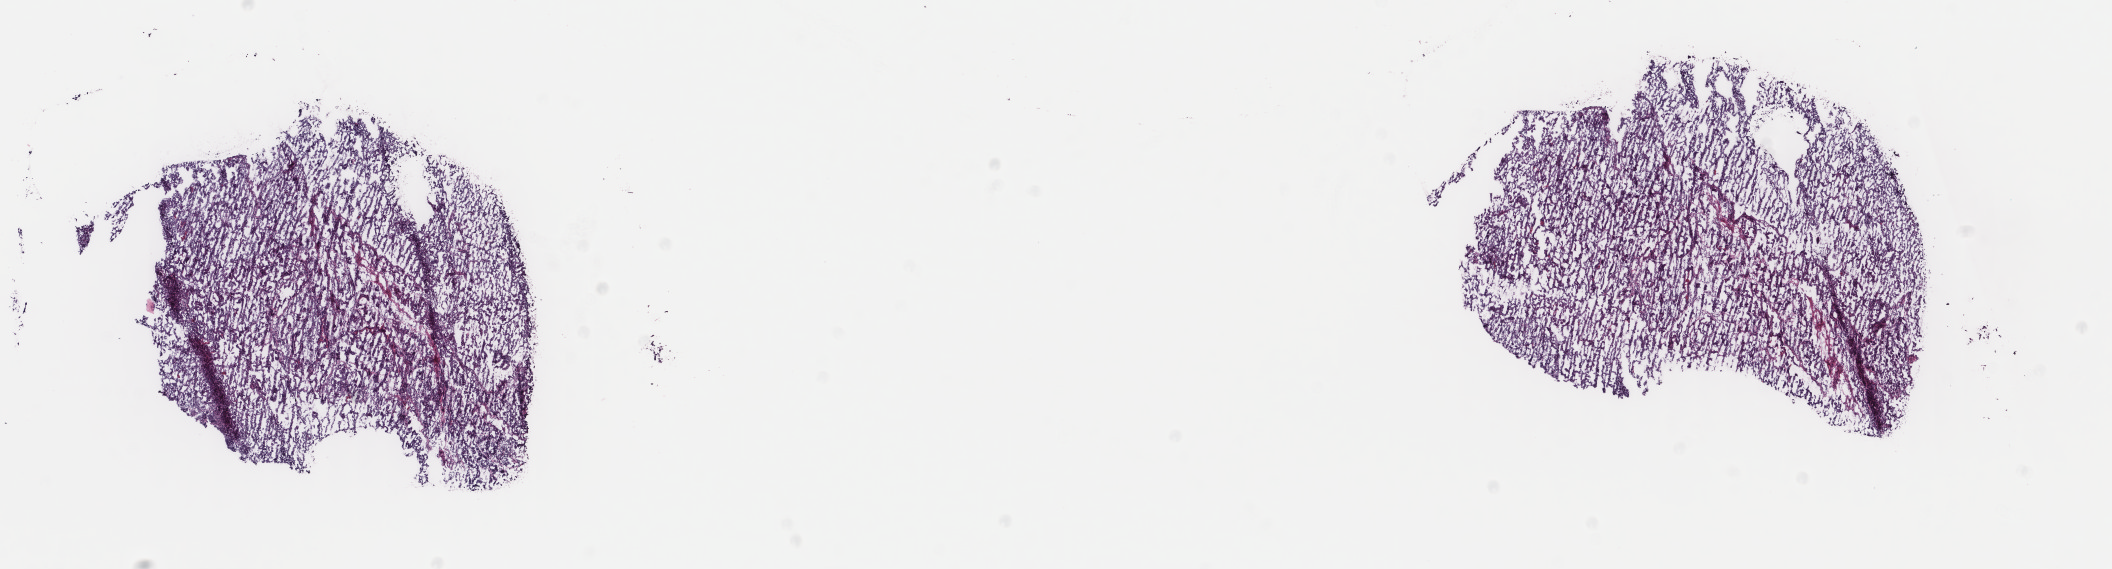
H&E whole-slide image, whole scanned area (about 16.8 x 4.5 mm, slide scanned at 40x) shown as a low-resolution overview; frozen section; sample: primary tumour, uterus. Female, age 55 years at initial diagnosis. Histologic grade: G3 (poorly differentiated). Composition of this section per pathologist review: tumour cells 80%, tumour nuclei 80%, normal cells 0%, stromal cells 10%, necrosis 10%. Infiltration values recorded for this section: lymphocyte infiltration 40%, monocyte infiltration 20%, neutrophil infiltration 20%.
Pathologic diagnosis: Endometrioid adenocarcinoma, NOS (endometrium). FIGO stage: IIB.